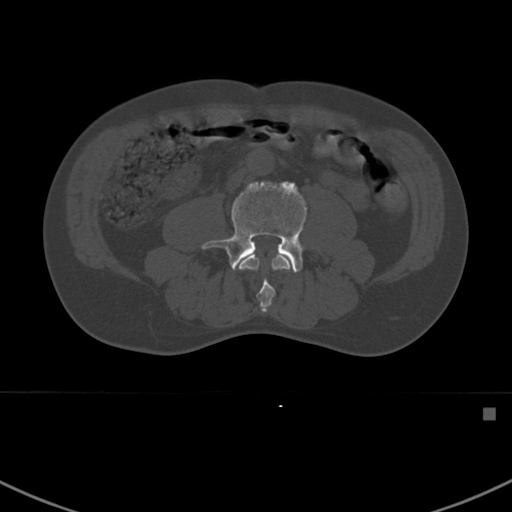
CT including the spine, one axial slice. Slice 249 of 412 in the series (ordered by position). Reconstruction kernel Br40s. 120 kVp. Bone window (W 1800 / L 400 HU). 512 × 512 image matrix, field of view 358 × 358 mm. Male patient, age 59 years. From the clinical record (not read from this slice): primary cancer: prostate.
Structures marked on this image (semi-automatic segmentation, software-assisted and operator-edited):
- L3 vertebra: bounding box (x1, y1, x2, y2) in pixels: (238, 253, 294, 313)
- L4 vertebra: (201, 181, 308, 272)